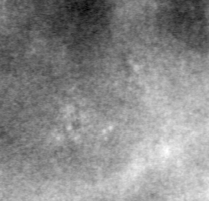
Crop from a digitized film mammogram around one marked abnormality, left breast, MLO view.
- Finding: calcifications, morphology pleomorphic, distribution clustered; BI-RADS assessment category 4; subtlety rating 1 on a 1 (subtle) to 5 (obvious) scale; pathology (as recorded): benign.